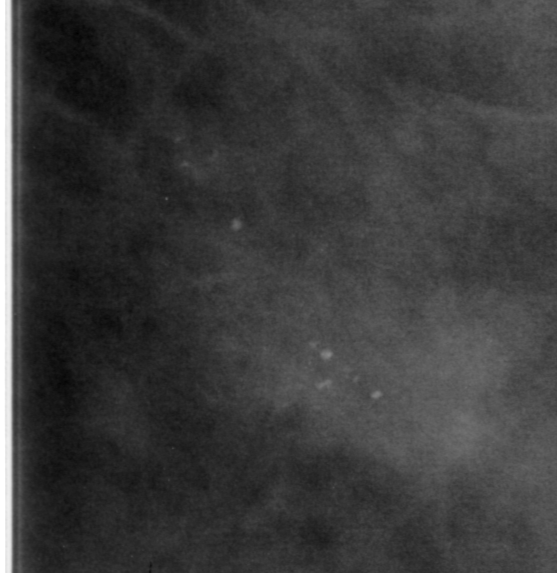
Region of interest cut from a scanned film mammogram (one marked finding); left breast; MLO view; BI-RADS breast density category 3 (scale 1–4).
- Calcifications, morphology round and regular / pleomorphic, distribution clustered; BI-RADS assessment category 0 (incomplete: needs additional imaging); subtlety rating 3 on a 1 (subtle) to 5 (obvious) scale; pathology result (as recorded, not read from the image): benign.